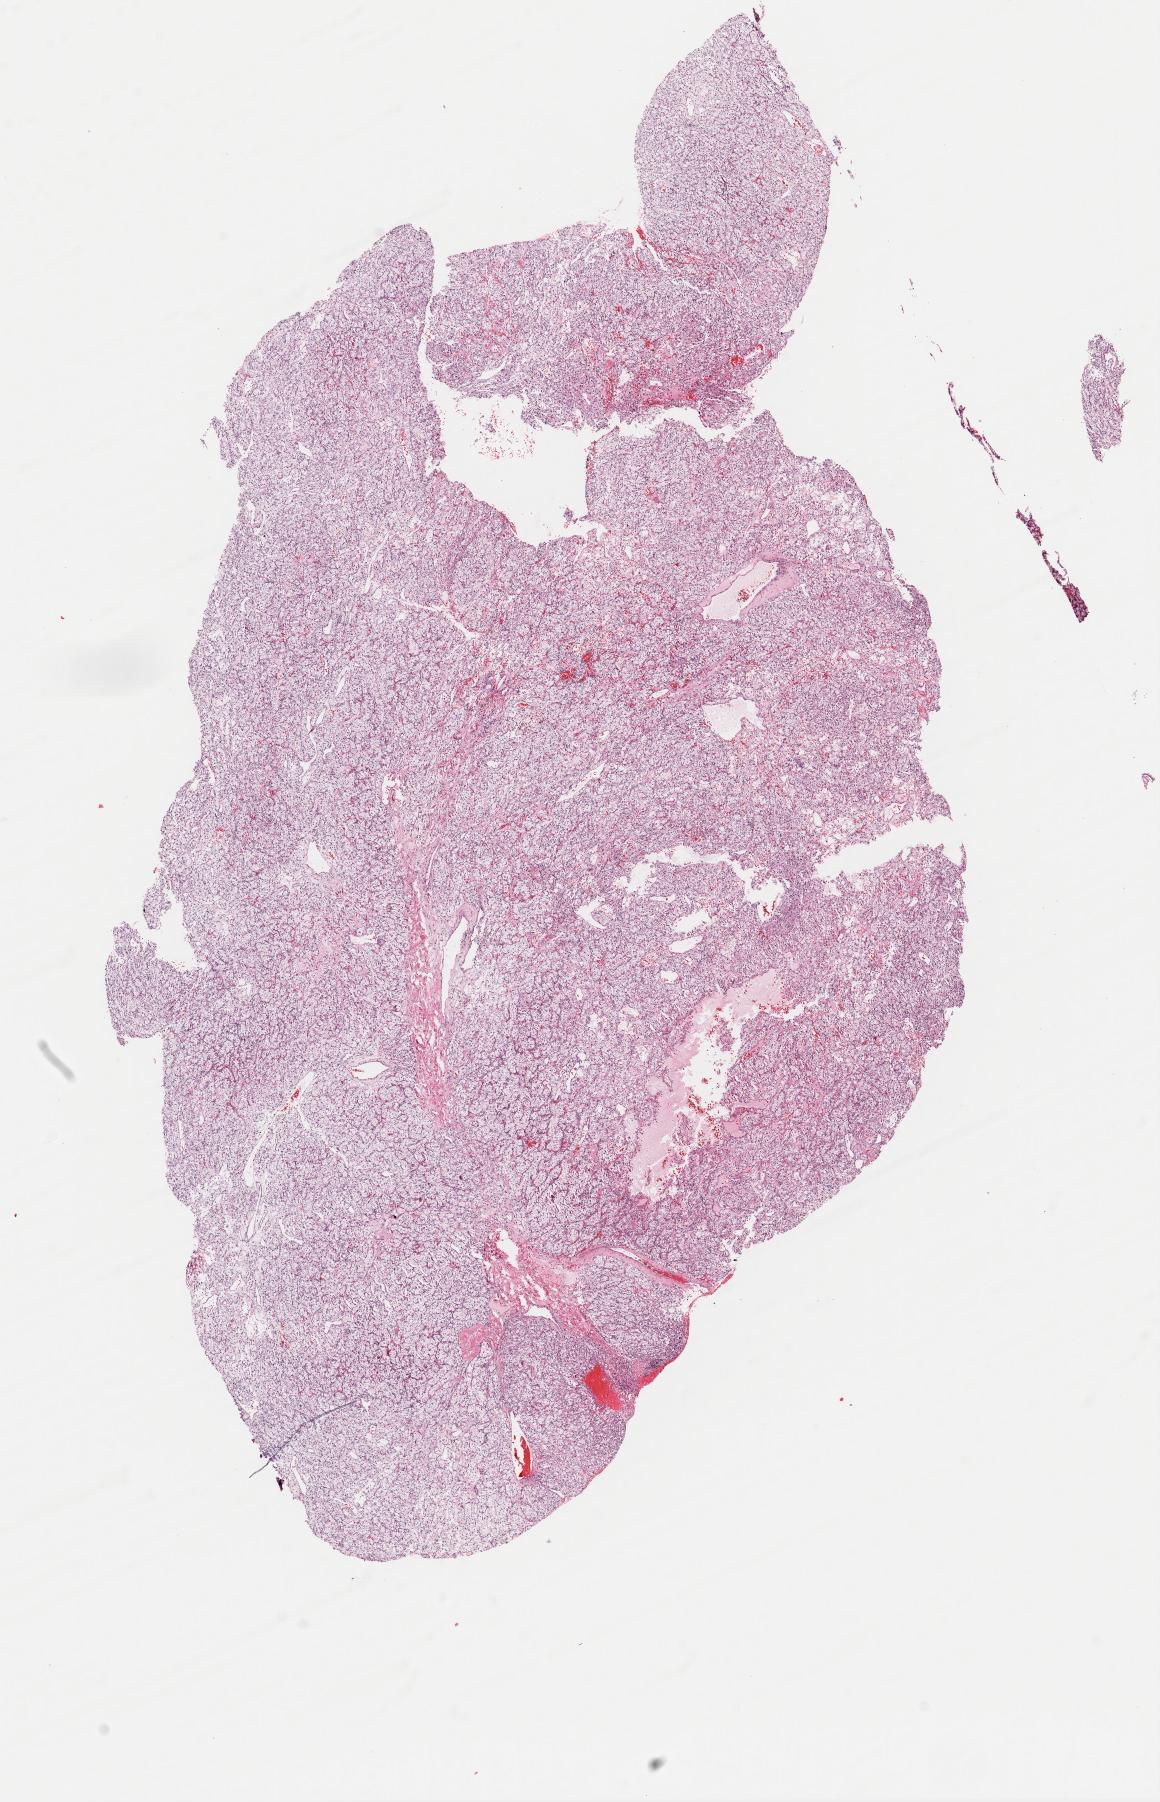
Digitized H&E tissue section (whole slide) — shown as a low-resolution overview of the whole scanned area (about 9.2 x 14.2 mm, acquisition: 40x scan); frozen section from the bottom of the tissue portion; primary tumour sample from the kidney. Male patient; age at initial diagnosis 73 years. Histologic grade: G2 (moderately differentiated). Slide review estimates, as recorded: tumour cells 82%, tumour nuclei 95%, normal cells 0%, stromal cells 18%, necrosis 0%. Infiltration values recorded for this section: lymphocyte infiltration 2%, monocyte infiltration 0%, neutrophil infiltration 0%.
* histologic diagnosis: Clear cell adenocarcinoma, NOS
* AJCC pathologic stage: I